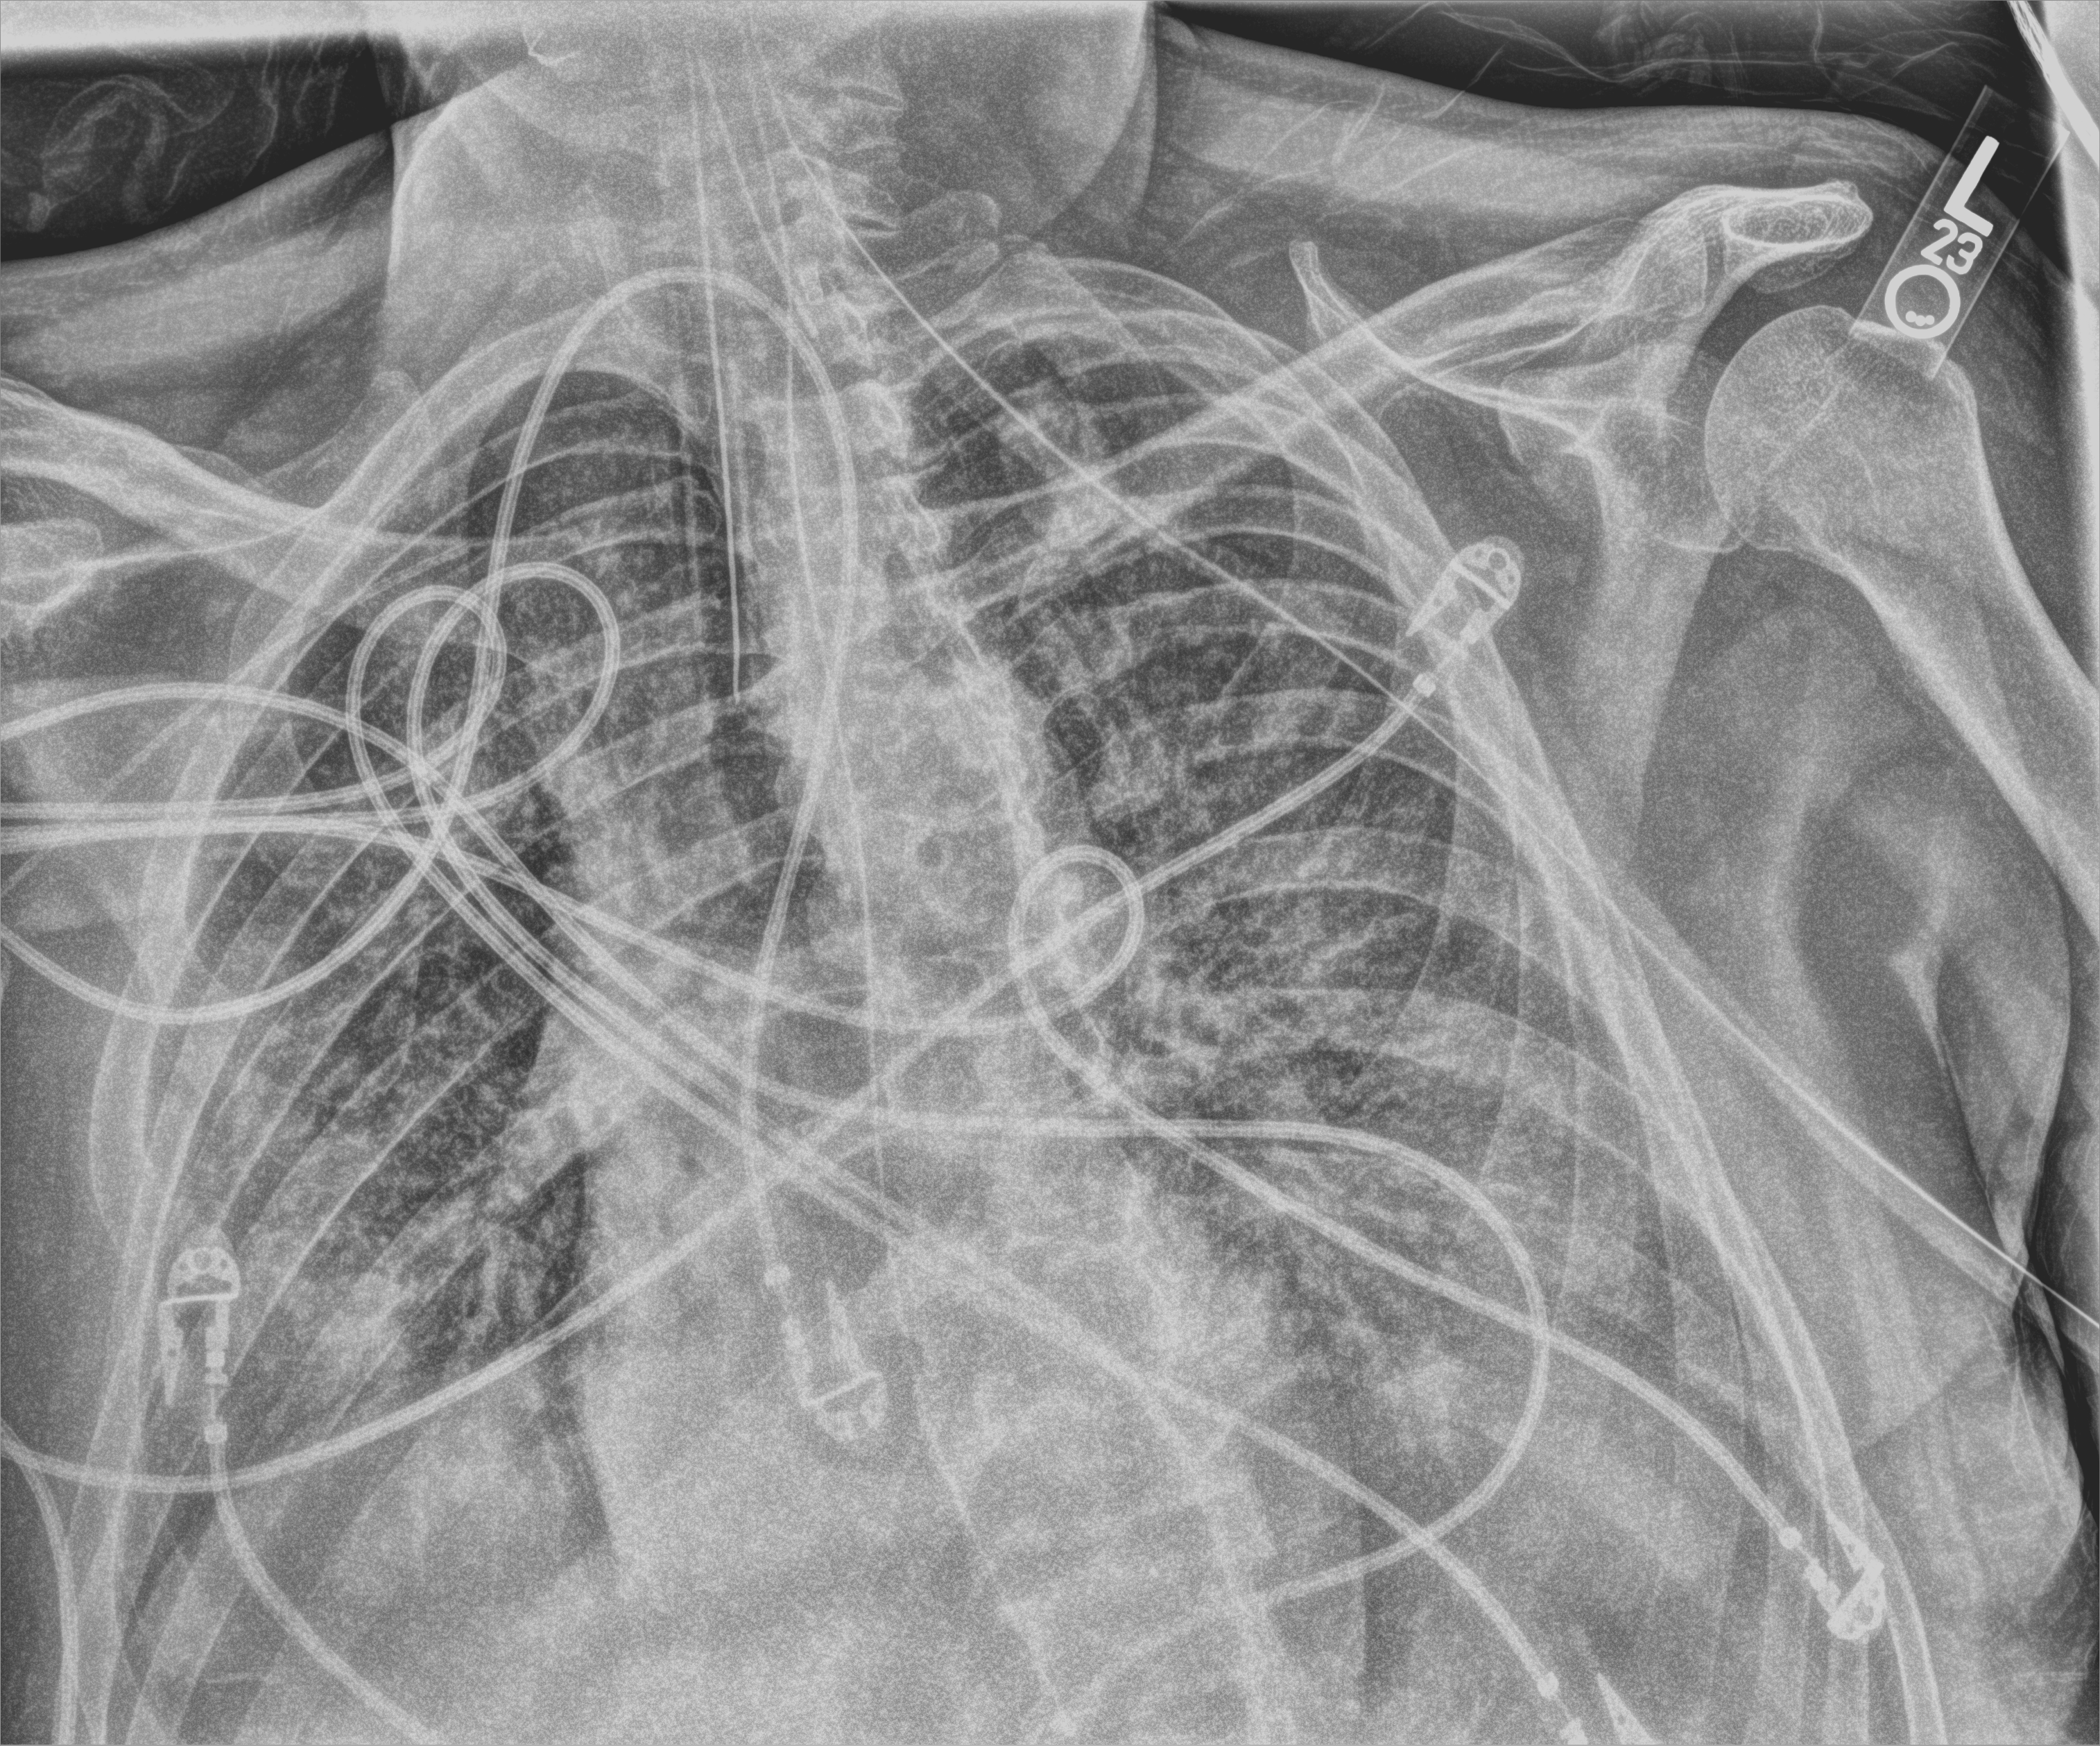
Portable chest radiograph, anteroposterior (AP) projection. Male patient hospitalised with COVID-19, age 60–74 years.
From the hospital-stay record, not from the radiograph (when in the stay this image was taken is not recorded): other chronic lung disease (admission record): no; mechanically ventilated during this hospital stay: yes; chronic kidney disease (admission record): no.